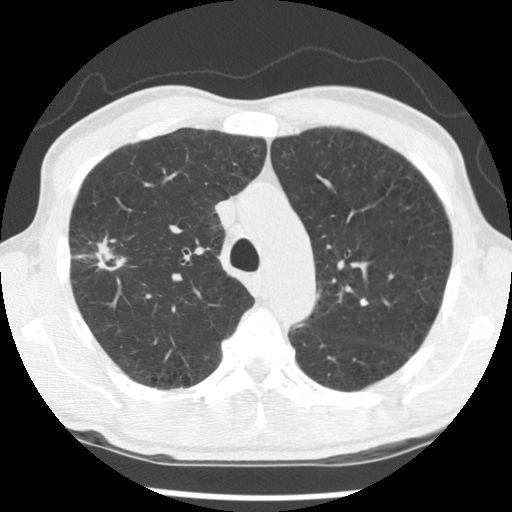
Axial slice from a low-dose chest CT screening exam; second screening round (one year after baseline); lung window (W 1500 / L -600 HU); 2.5 mm slice thickness; standard (soft-tissue) reconstruction kernel (STANDARD). Male, age 56 years at enrolment.
• Expert reader's lesion annotation, box from (x=56, y=231) to (x=141, y=297) px.
• The exam's reader record, not a measurement of the box and not confirmed to be the same lesion: non-calcified nodule or mass ≥4 mm, right upper lobe, 30 × 18 mm, spiculated (stellate) margins, mixed attenuation, pre-existing on the prior screen: yes; interval growth: yes.
• Later outcome: lung cancer diagnosed 326 days after this screen — squamous cell carcinoma, NOS, right upper lobe, right middle lobe, moderately differentiated (G2), stage IB (AJCC 6th edition), 70 mm at pathology.